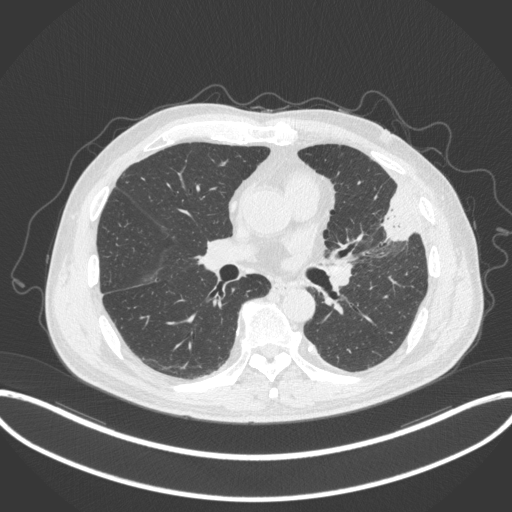
Chest CT, one axial slice. Slice 174 of 382 in the series (ordered by position). Reconstruction kernel B31f. 120 kVp. Lung window (W 1500 / L -600 HU). 1 mm slice thickness. 512 × 512 image matrix, field of view 415 × 415 mm. Male patient, age 64 years. From the clinical record (not read from this slice): clinical TNM (as recorded): T4 N1 M0; histopathological grade: G3.
Outlined on this slice (bounding box drawn by a radiologist):
- lung tumour (recorded histology: adenocarcinoma): box from (x=371, y=182) to (x=416, y=243) px